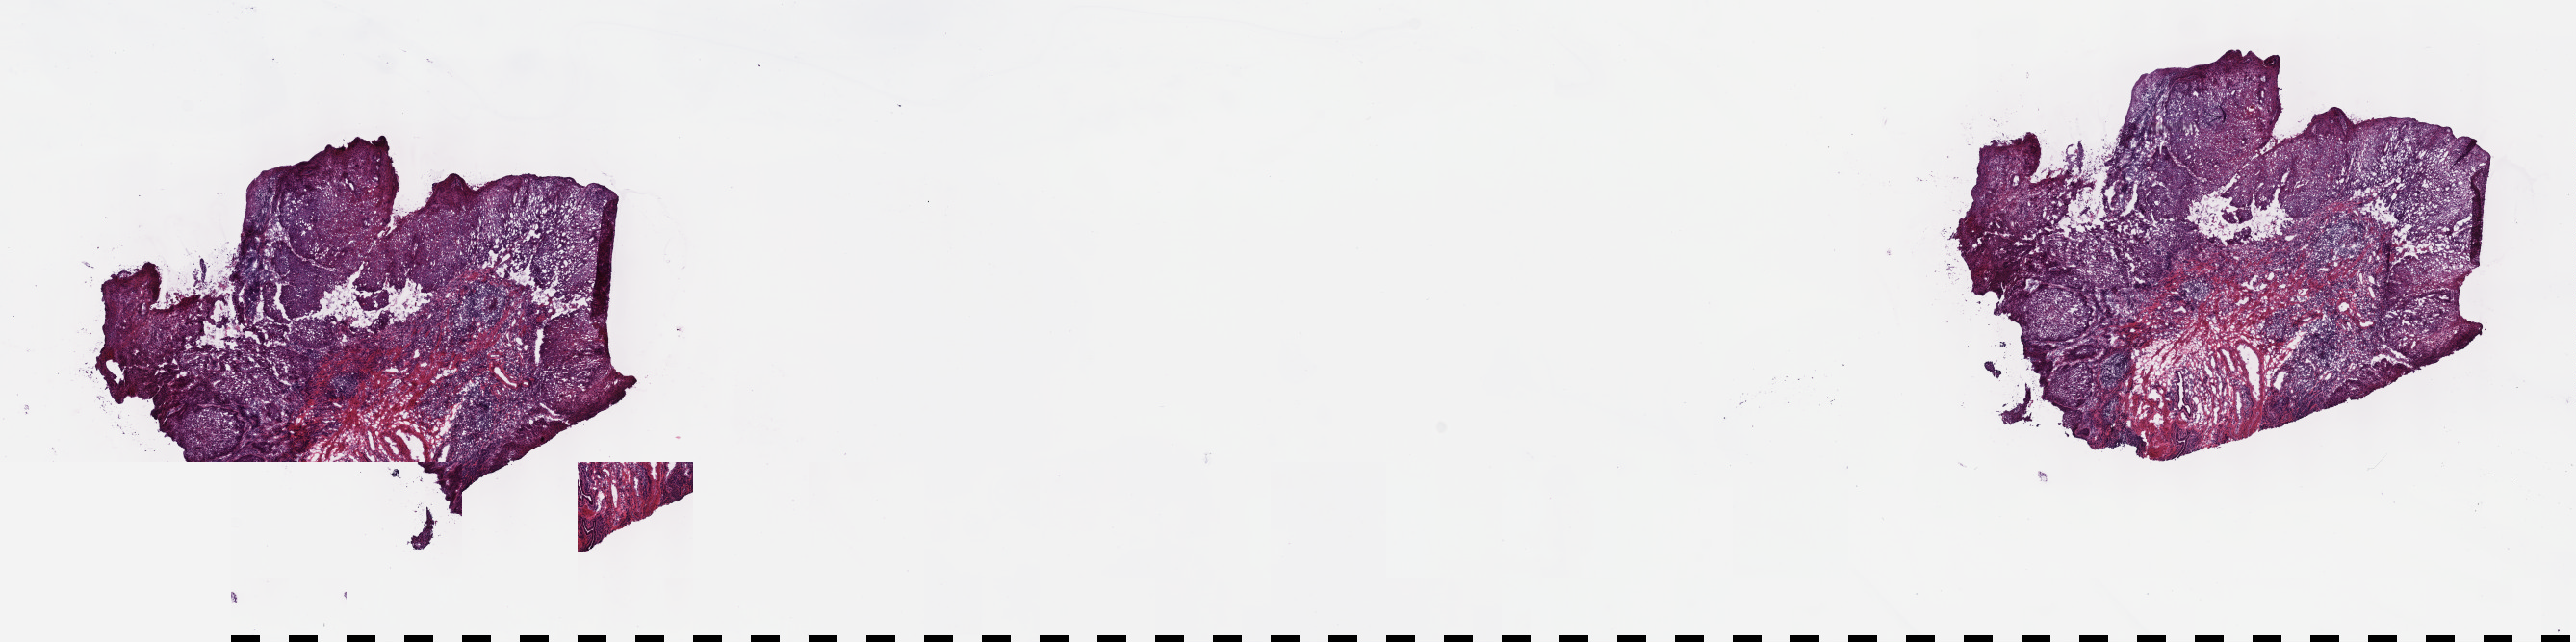
Whole-slide histology image, H&E, shown as a low-resolution overview of the whole scanned area (about 21.6 x 5.4 mm). Frozen section from the top of the tissue portion. Primary tumour sample from the esophagus. Patient: male, age at initial diagnosis 63 years. Histologic grade: G2 (moderately differentiated). Composition of this section per pathologist review: tumour cells 100%, tumour nuclei 75%, normal cells 0%, stromal cells 0%, necrosis 0%. Inflammatory infiltration, as recorded: lymphocyte infiltration 4%, monocyte infiltration 0%, neutrophil infiltration 0%.
AJCC pathologic stage: IVA. Diagnosis: Squamous cell carcinoma, NOS (middle third of esophagus). TNM: T1 N1 M1a. Lymph nodes positive (case pathology): 9 of 34 examined.